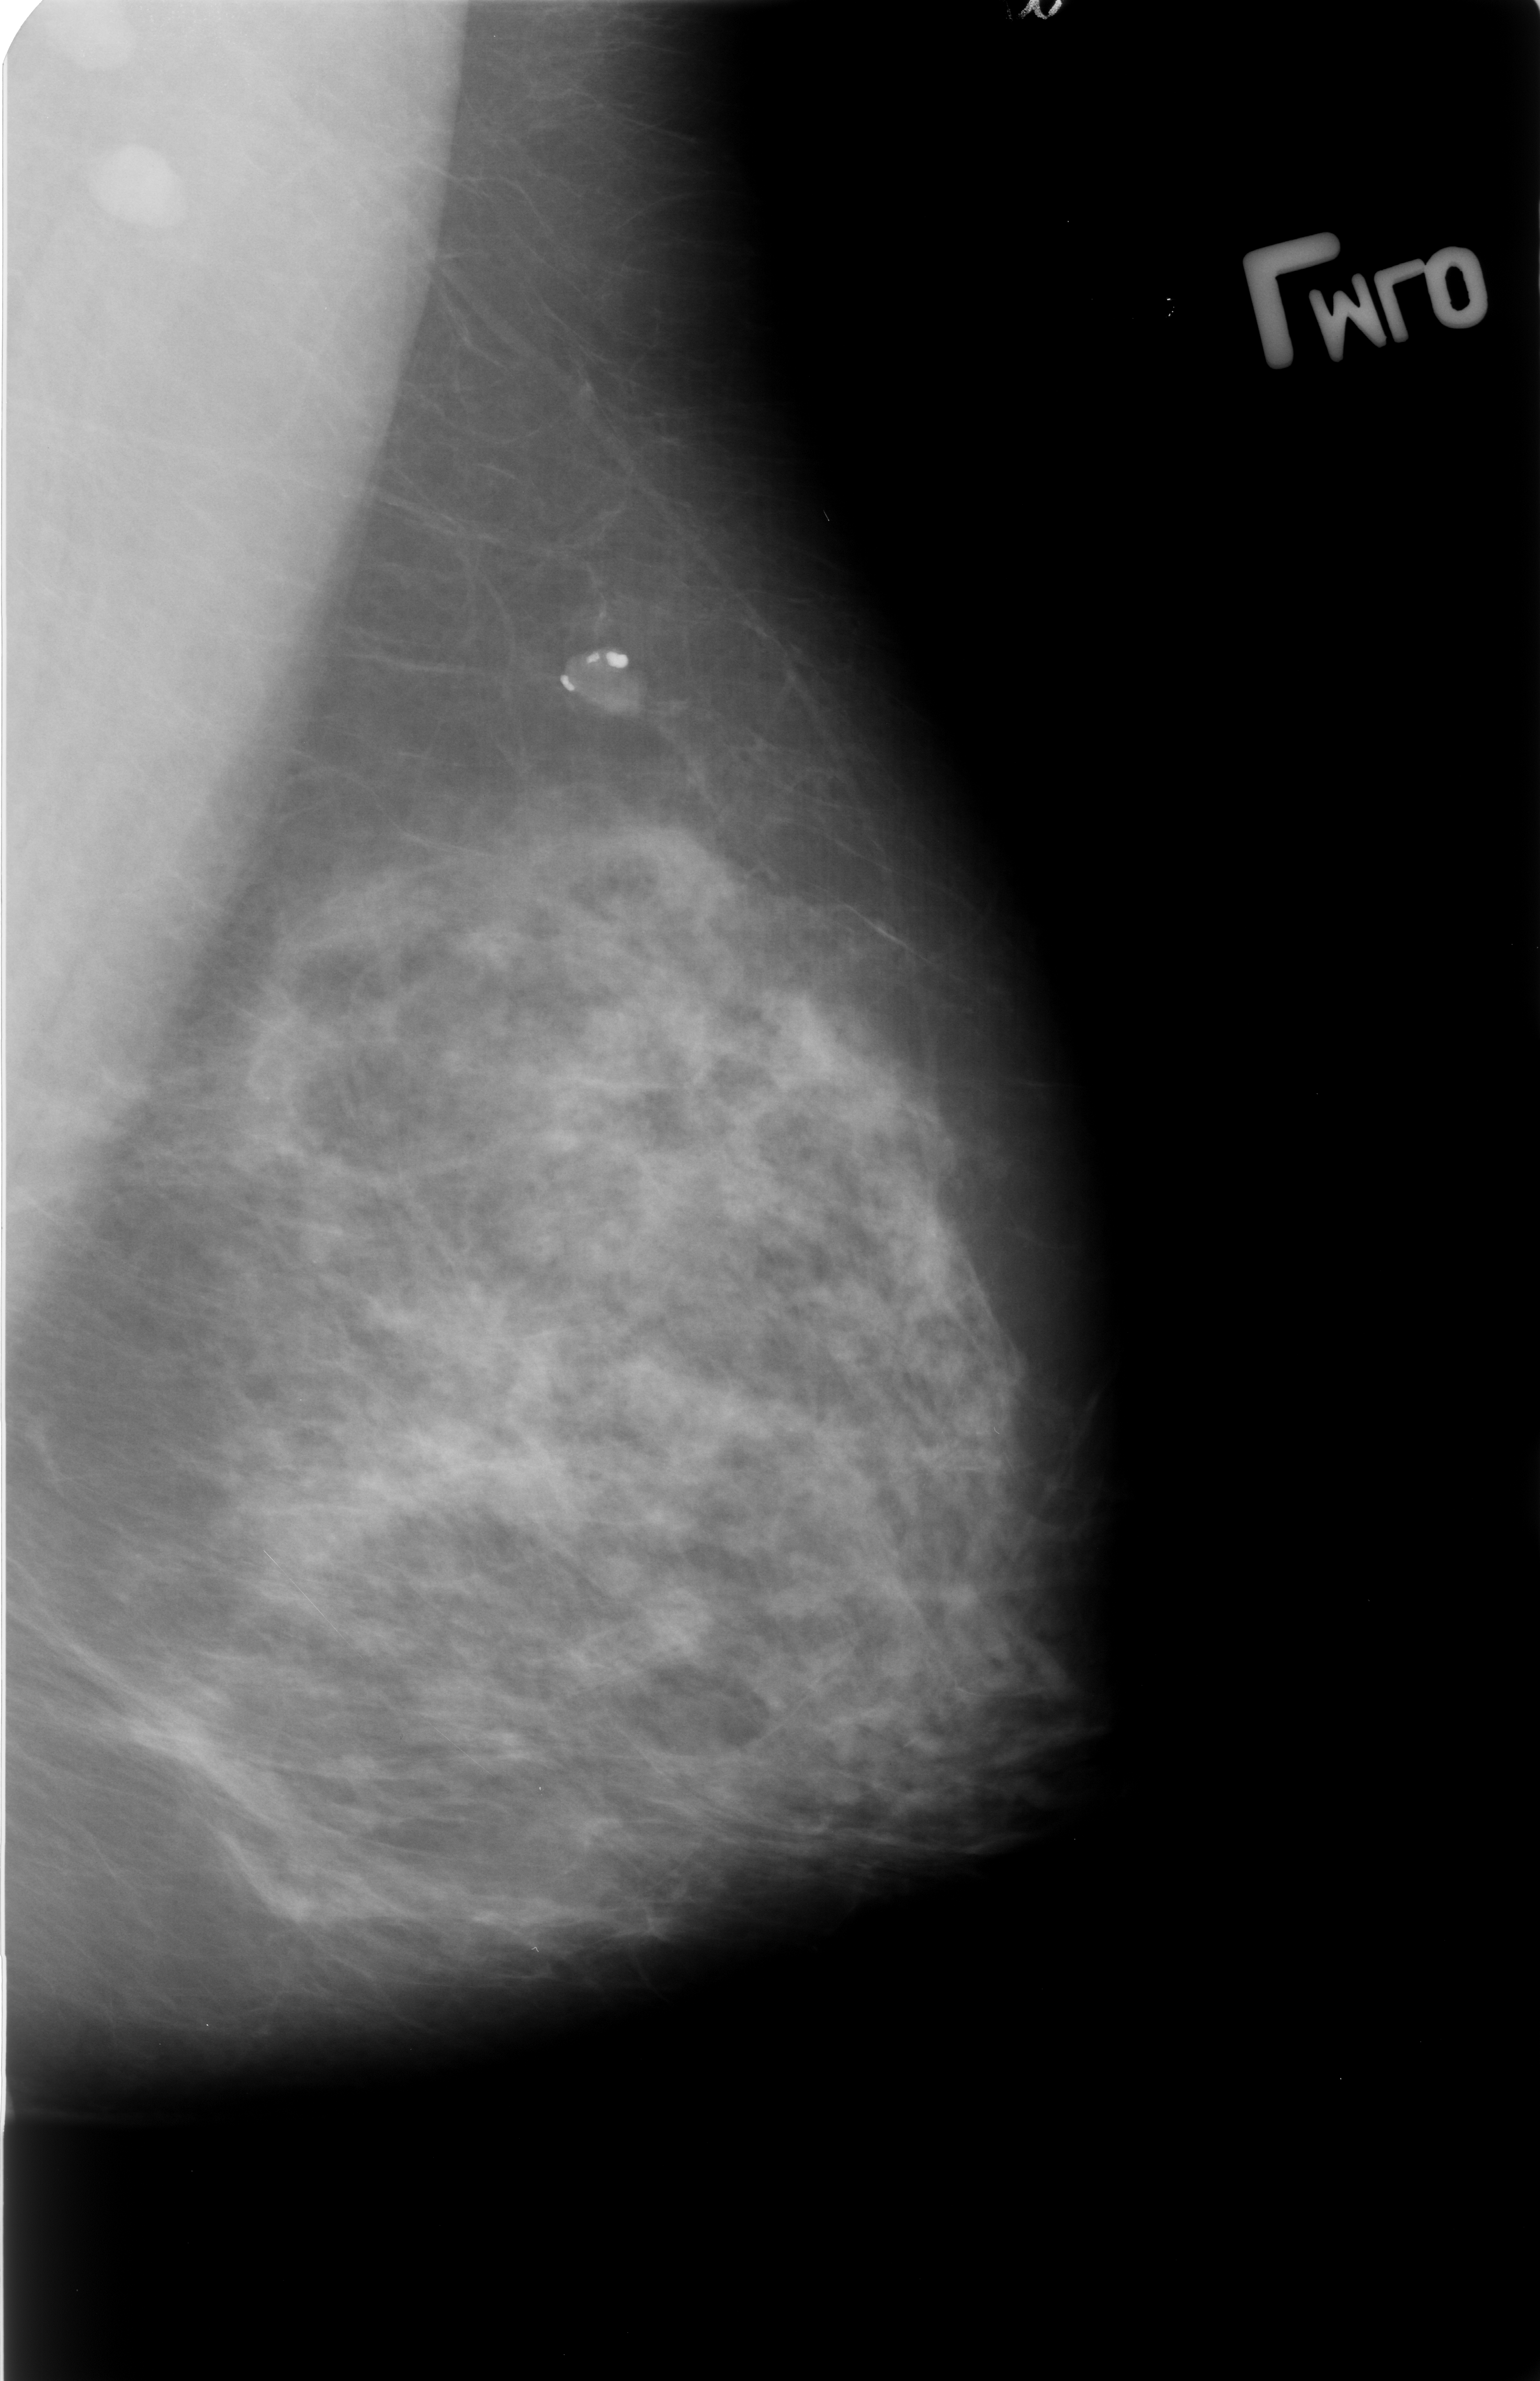
Mammogram (digitized film), left breast, mediolateral oblique (MLO) view, breast composition: heterogeneously dense (BI-RADS density category 3 of 4).
Marked abnormality: calcifications, morphology coarse; BI-RADS assessment category 2; subtlety rating 3 on a 1 (subtle) to 5 (obvious) scale; benign; no additional work-up was recommended (benign without callback).